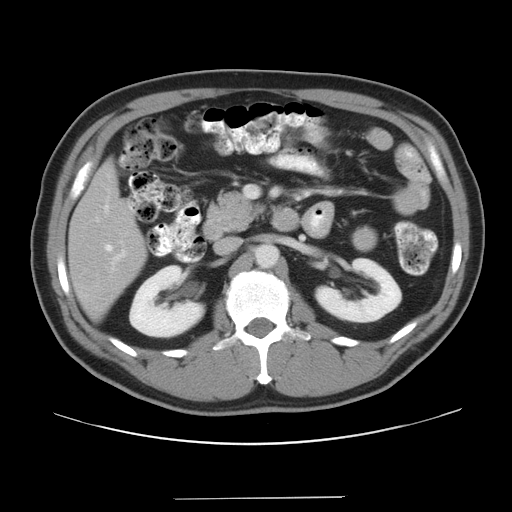
Contrast-enhanced abdominal CT, one axial slice. Position 17 of 37 along the scan axis. 120 kVp. Soft-tissue window (W 400 / L 40 HU). 7.5 mm slice thickness. 512 × 512 image matrix. Male patient, age 46 years. From the clinical record (not read from this slice): diagnosis: colorectal cancer liver metastases, imaged before liver resection; multiple liver metastases: yes.
Annotated regions visible in this slice (outlined manually by an expert reader):
- hepatic veins: box from (x=105, y=244) to (x=112, y=251) px
- liver: (x=71, y=167)–(x=145, y=317)
- planned liver remnant (the part of the liver to remain after resection): (x=71, y=167)–(x=145, y=317)
- portal vein (with intrahepatic branches): (x=117, y=251)–(x=125, y=258)